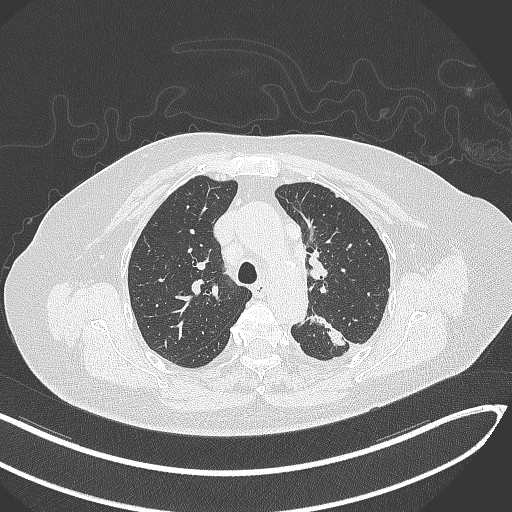
Chest CT, one axial slice; slice 223 of 270 in the series (ordered by position); reconstruction kernel B70f; 120 kVp; lung window (W 1500 / L -600 HU); 512 × 512 image matrix, field of view 400 × 400 mm. Female patient, age 76 years. Case-level facts recorded for this patient, not image findings: clinical TNM (as recorded): T1c N0 M0.
Annotated regions visible in this slice (rectangle marked by the reading radiologist):
- lung tumour (recorded histology: adenocarcinoma): bounding box <306,315,350,354> (left, top, right, bottom; pixels)